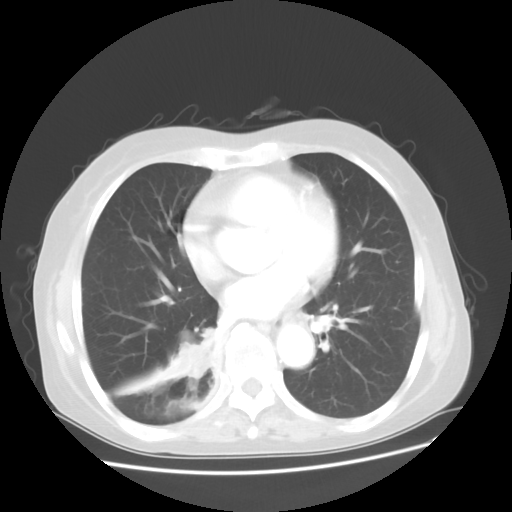
Chest CT, one axial slice. Slice 19 of 48 in the series (ordered by position). Lung window (W 1500 / L -600 HU). 5 mm slice thickness. 512 × 512 image matrix. Patient: female, 63 years. From the clinical record (not read from this slice): clinical TNM (as recorded): T2 N3 M1b; histopathological grade: G3.
Outlined on this slice (bounding box drawn by a radiologist):
- lung tumour (recorded histology: small cell carcinoma): bounding box [x1, y1, x2, y2] px = [170, 340, 214, 390]